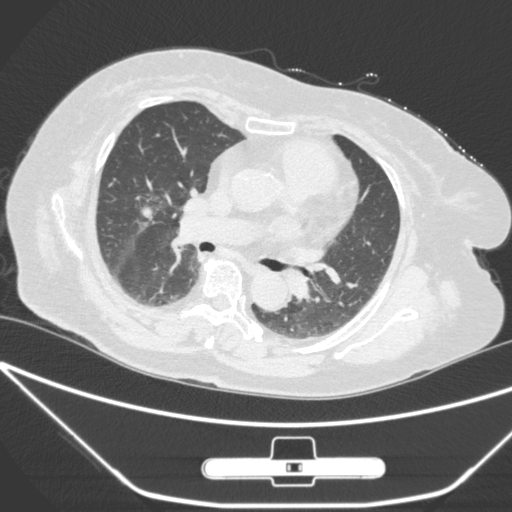
Chest CT, one axial slice; slice 152 of 245 in the series (ordered by position); lung window (W 1500 / L -600 HU); 1 mm slice thickness; 512 × 512 image matrix, field of view 365 × 365 mm. Female patient, age 65 years. Case-level facts recorded for this patient, not image findings: clinical TNM (as recorded): T1c N0 M0; histopathological grade: G3.
Structures marked on this image (bounding box drawn by a radiologist):
- lung tumour (recorded histology: adenocarcinoma): bounding box <132,201,166,236> (left, top, right, bottom; pixels)